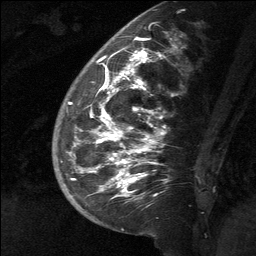
Breast MRI (dynamic contrast-enhanced), one sagittal slice; position 23 of 64 along the scan axis; dynamic contrast-enhanced study with each time point stored as its own series, time point 2 of 3 at this slice position (early post-contrast, ordered by acquisition time); 1.5 T; TE 4.8 ms, TR 27 ms; 2 mm slice thickness; 256 × 256 image matrix, field of view 180 × 180 mm. Female patient, age 39 years. Case-level facts recorded for this patient, not image findings: setting: breast cancer imaged before/during neoadjuvant chemotherapy; receptor status: HER2-positive.
Annotated regions visible in this slice (semi-automatically segmented with operator editing):
- analysis volume of interest (the breast-tissue region the enhancement analysis was run in; not a lesion): bounding box <58,40,201,217> (left, top, right, bottom; pixels)
- tumour enhancement mask (voxels above the 90 % enhancement threshold inside the analysis volume of interest): <69,50,163,196>